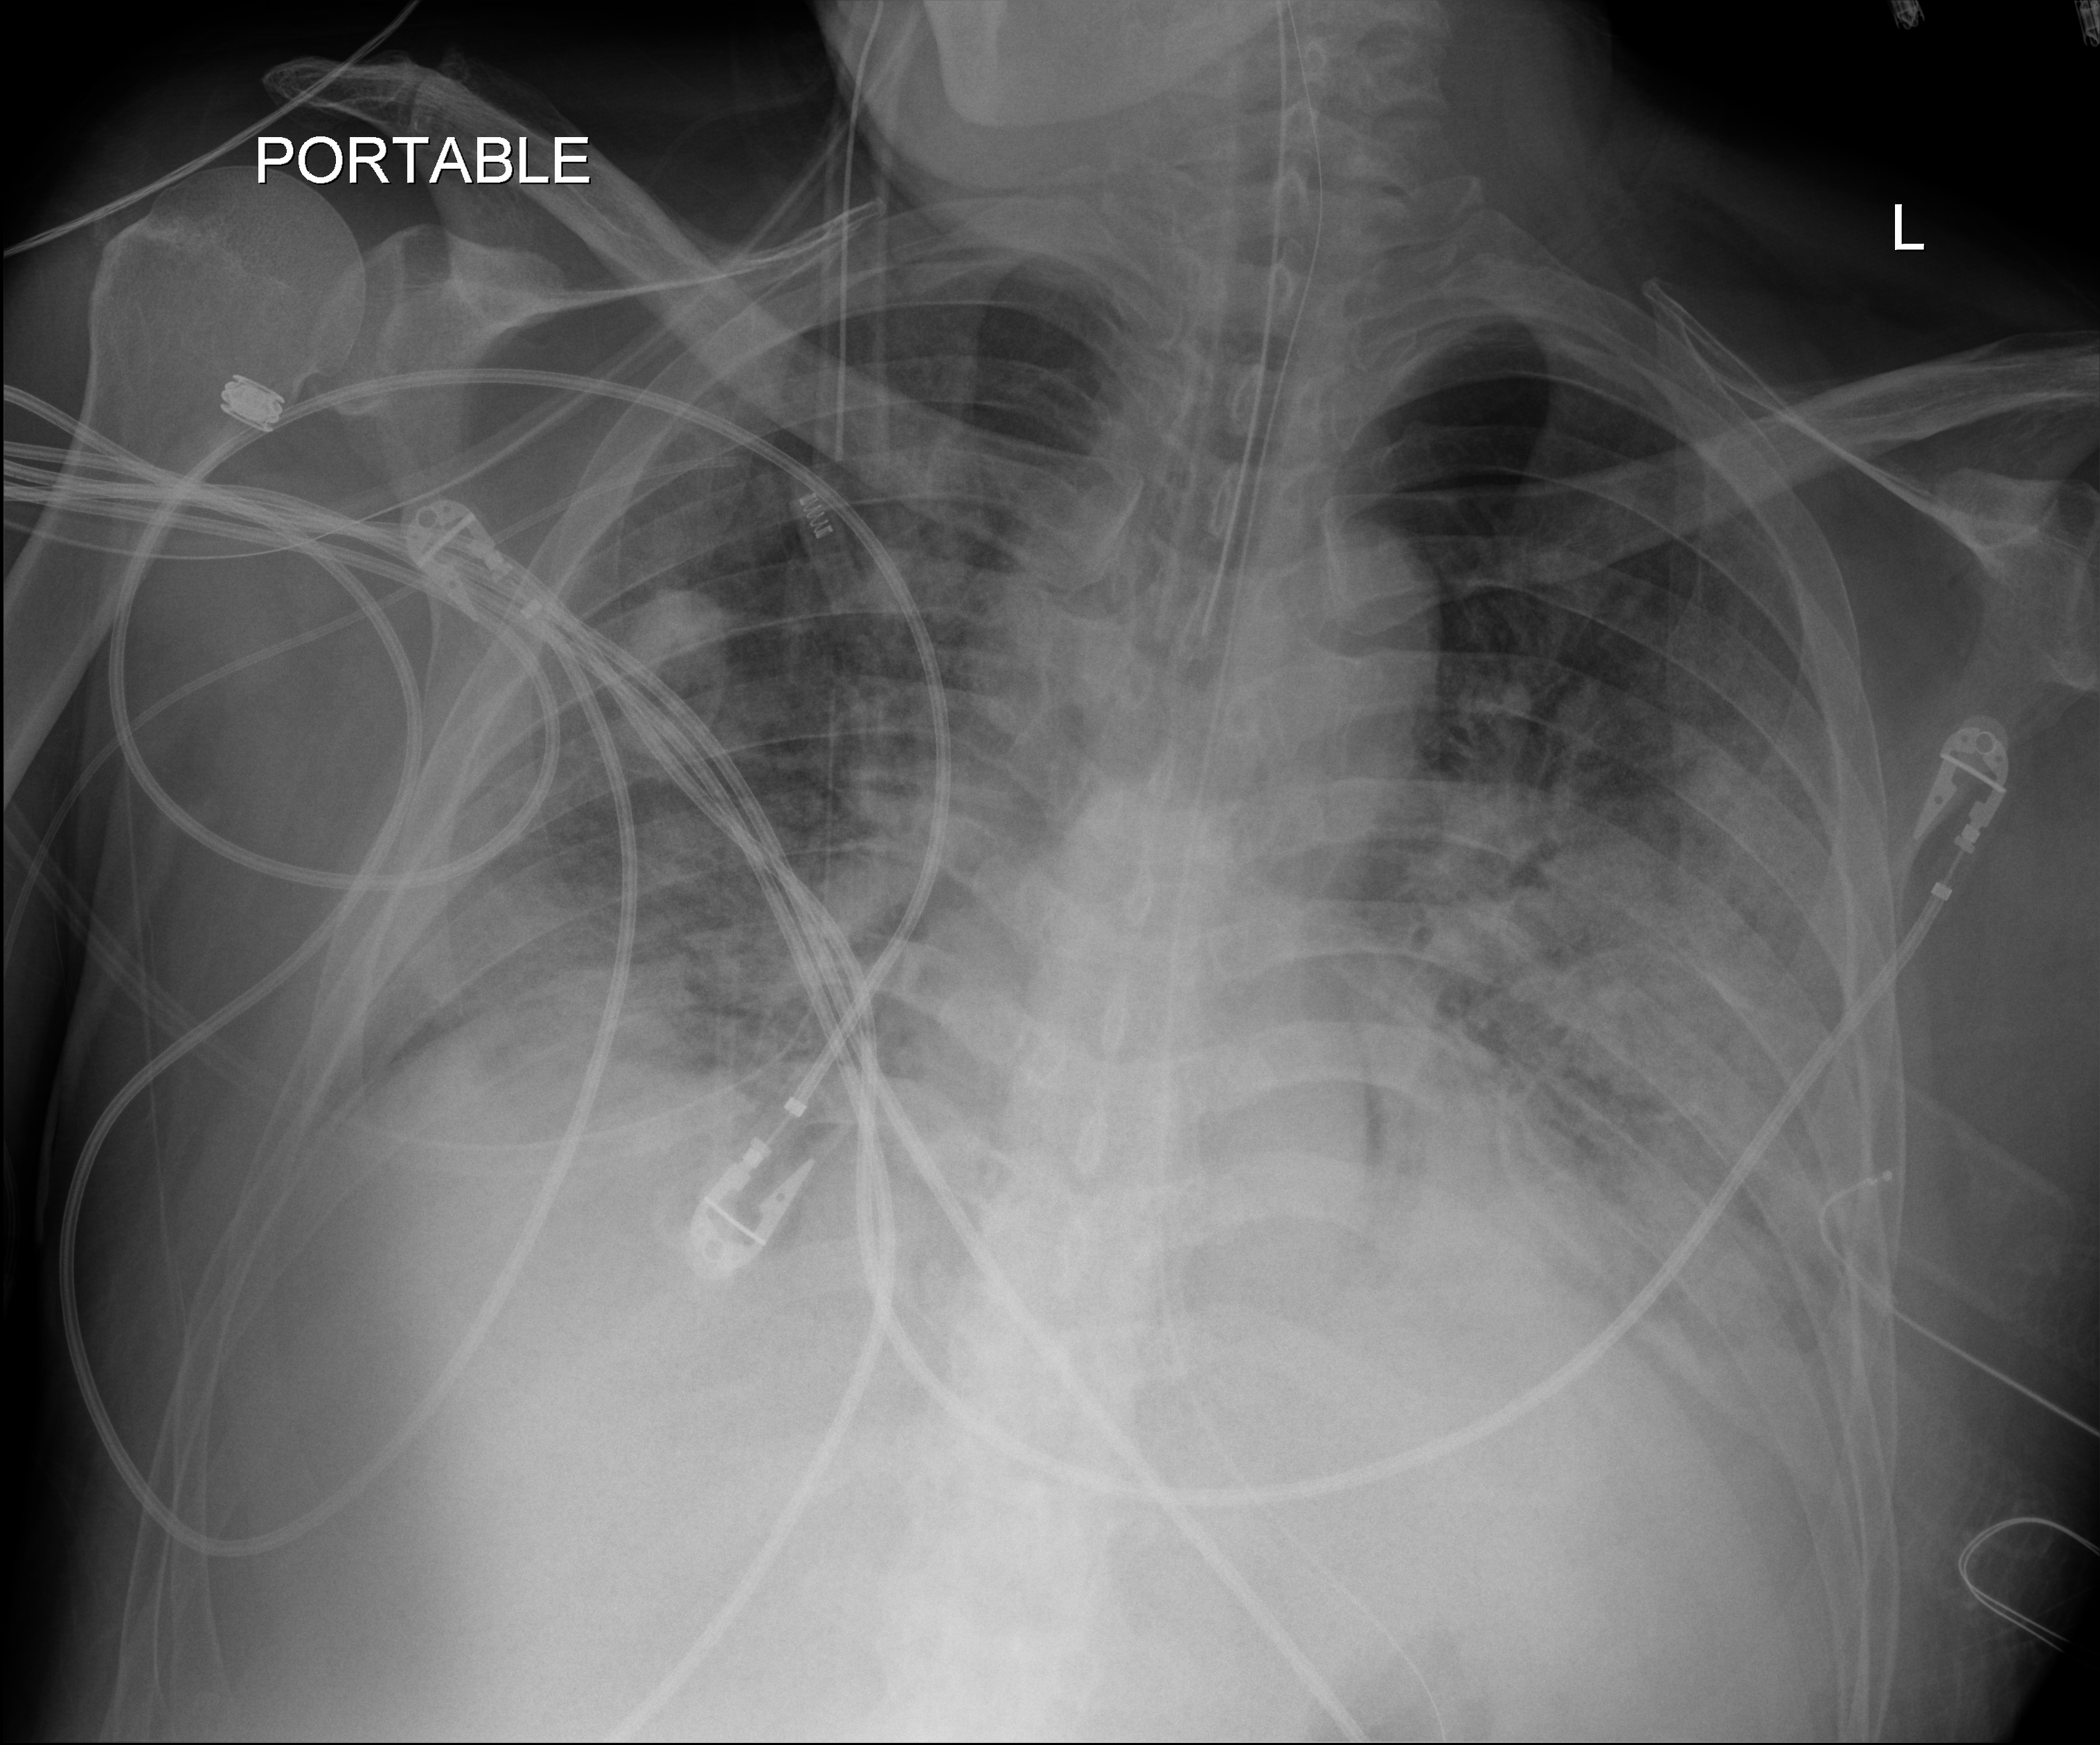
Portable chest radiograph; anteroposterior (AP) projection. Male patient hospitalised with COVID-19, age 18–59 years.
Admission-level facts for this patient (not findings on this image; timing relative to this image not recorded):
- COPD (admission record): no
- admitted to intensive care during this hospital stay: yes
- length of hospital stay: 40 days